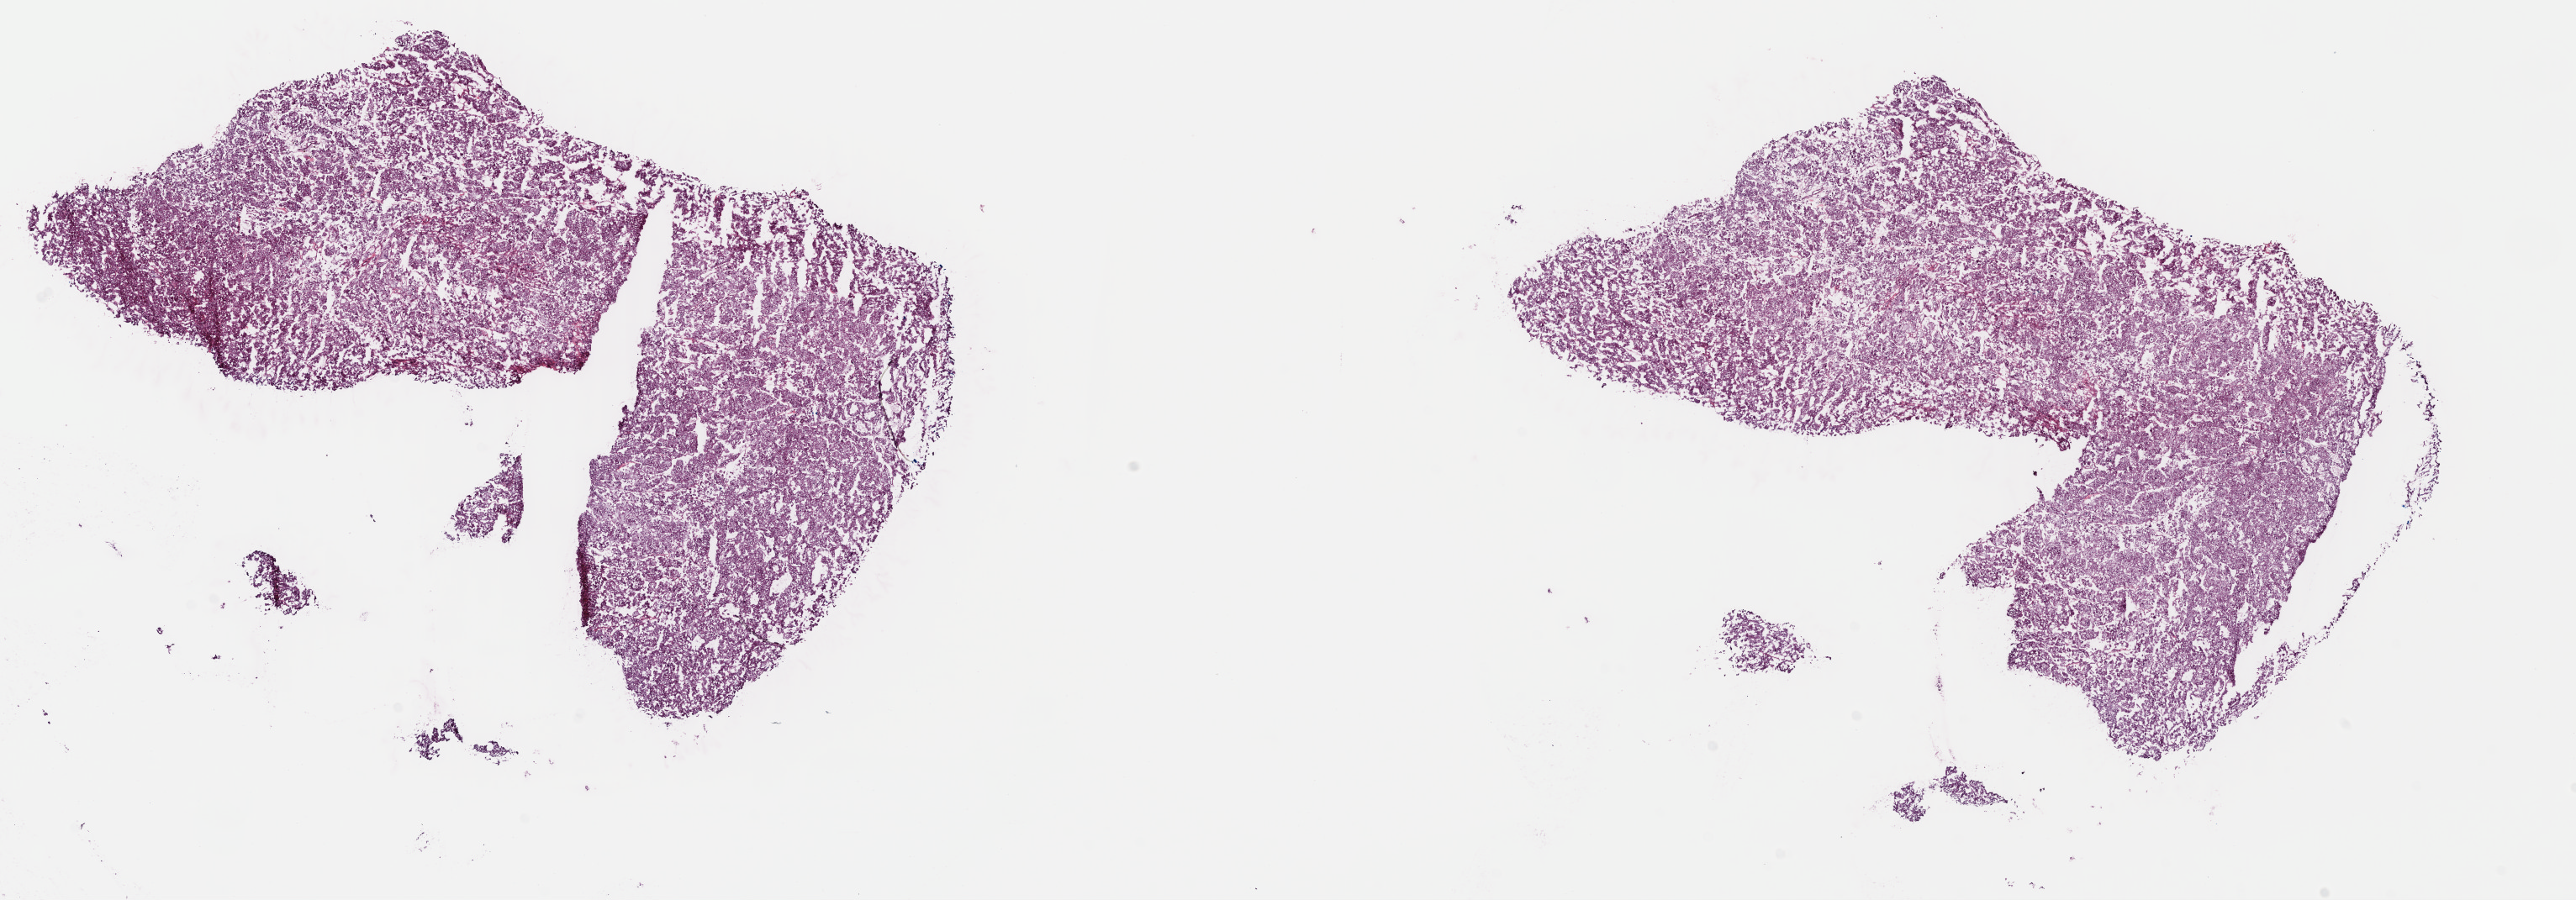
Whole-slide histology image, Hematoxylin and eosin (H&E) stained, low-resolution overview of the scanned area, about 24.1 x 8.4 mm, frozen section from the top of the tissue portion, sample: primary tumour, kidney. Male patient; age at initial diagnosis 52 years. Composition of this section per pathologist review: tumour cells 95%, tumour nuclei 95%.
Pathologic diagnosis: Renal cell carcinoma, chromophobe type.